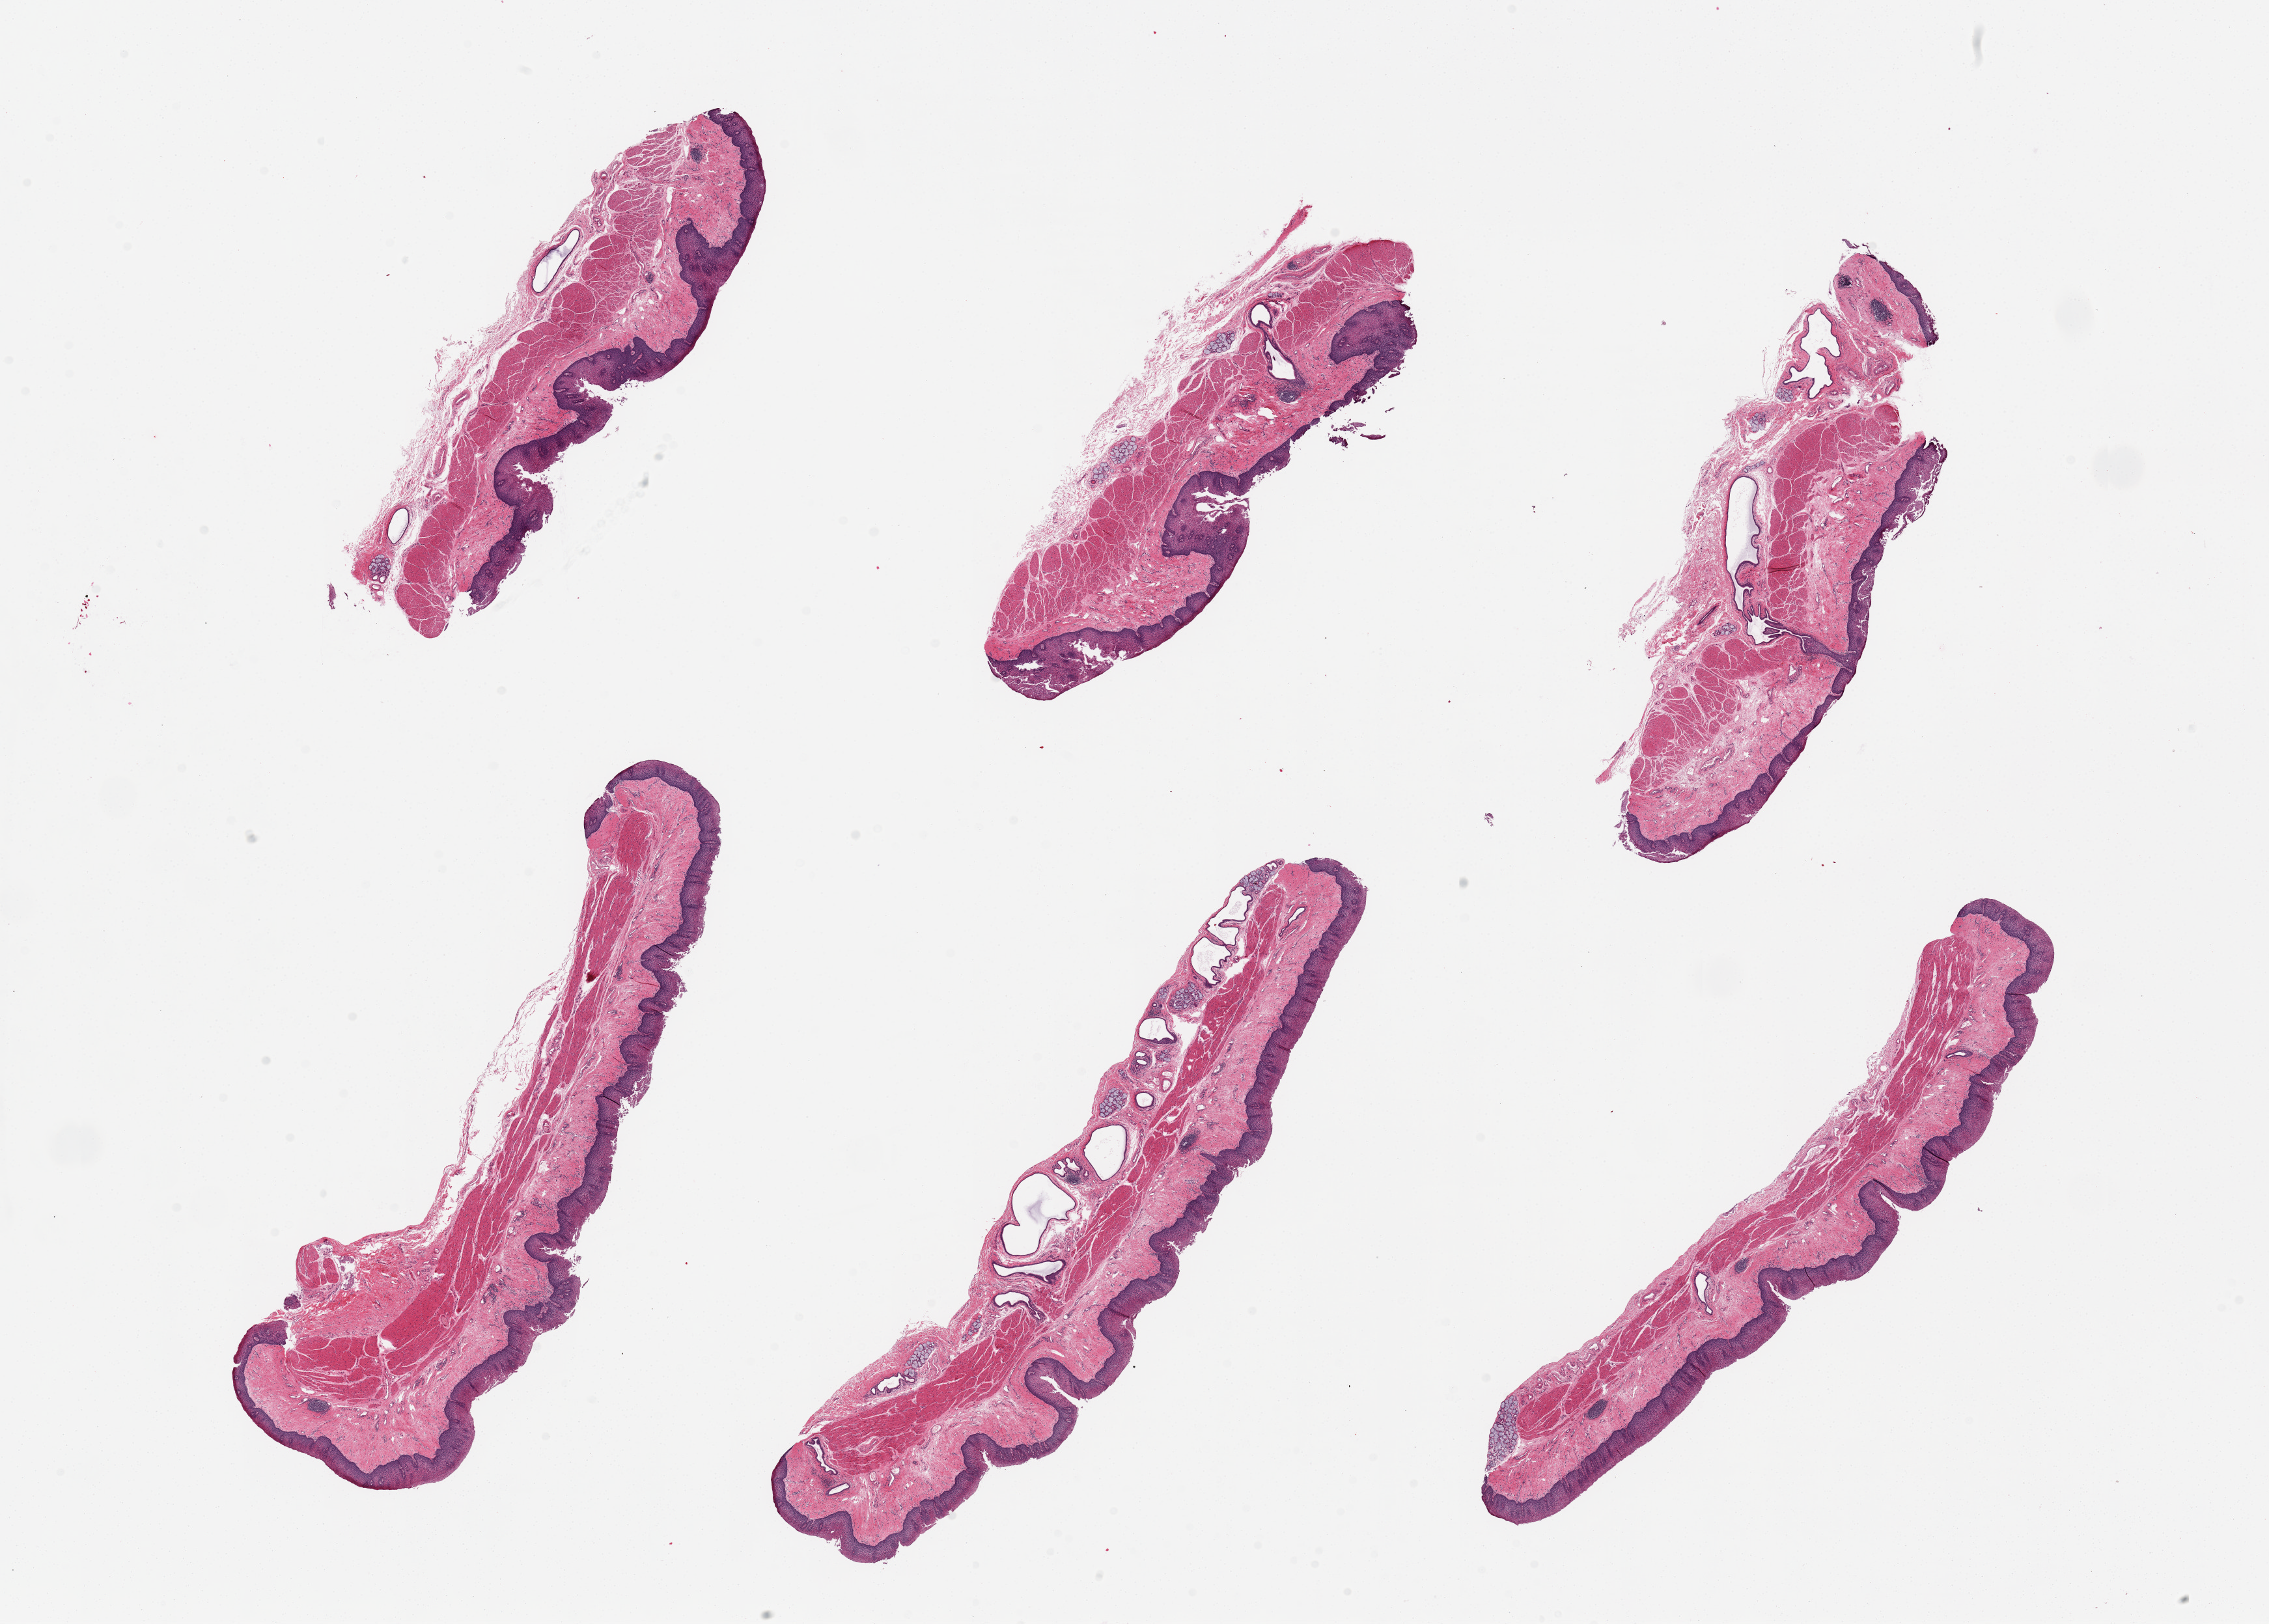
Digitized hematoxylin and eosin (H&E)-stained section — whole scanned area (about 27.6 x 19.7 mm, slide scanned at 20x) shown as a low-resolution overview; PAXgene-fixed, paraffin-embedded tissue; target tissue: esophageal mucous membrane; tissue donor sample. Donor: male.
- review note (as recorded): 1 piece; comparable to 25 block